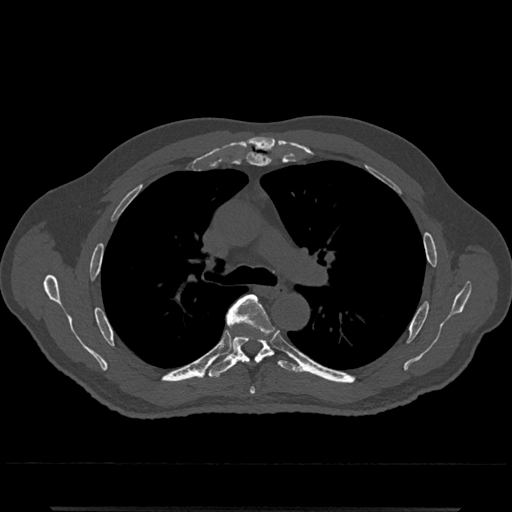
CT including the spine, one axial slice. Slice 796 of 797 in the series (ordered by position). Reconstruction kernel Br40s/3. 120 kVp. Bone window (W 1800 / L 400 HU). 0.5 mm slice thickness. 512 × 512 image matrix, field of view 393 × 393 mm. Patient: male, 67 years. Case-level facts recorded for this patient, not image findings: primary cancer: prostate.
Outlined on this slice (semi-automatic segmentation, software-assisted and operator-edited):
- T5 vertebra: bounding box <225,294,270,328> (left, top, right, bottom; pixels)
- T6 vertebra: <208,321,297,378>